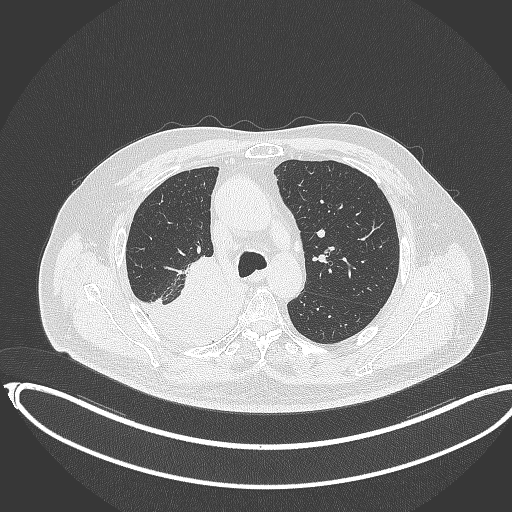
Chest CT, one axial slice; slice 247 of 403 in the series (ordered by position); reconstruction kernel B70f; 120 kVp; lung window (W 1500 / L -600 HU); 1 mm slice thickness; 512 × 512 image matrix, field of view 436 × 436 mm. Patient: male, 68 years. Case-level facts recorded for this patient, not image findings: clinical TNM (as recorded): T2a N0 M0.
Annotated regions visible in this slice (bounding box drawn by a radiologist):
- lung tumour (recorded histology: adenocarcinoma): bounding box [x1, y1, x2, y2] px = [123, 259, 243, 353]